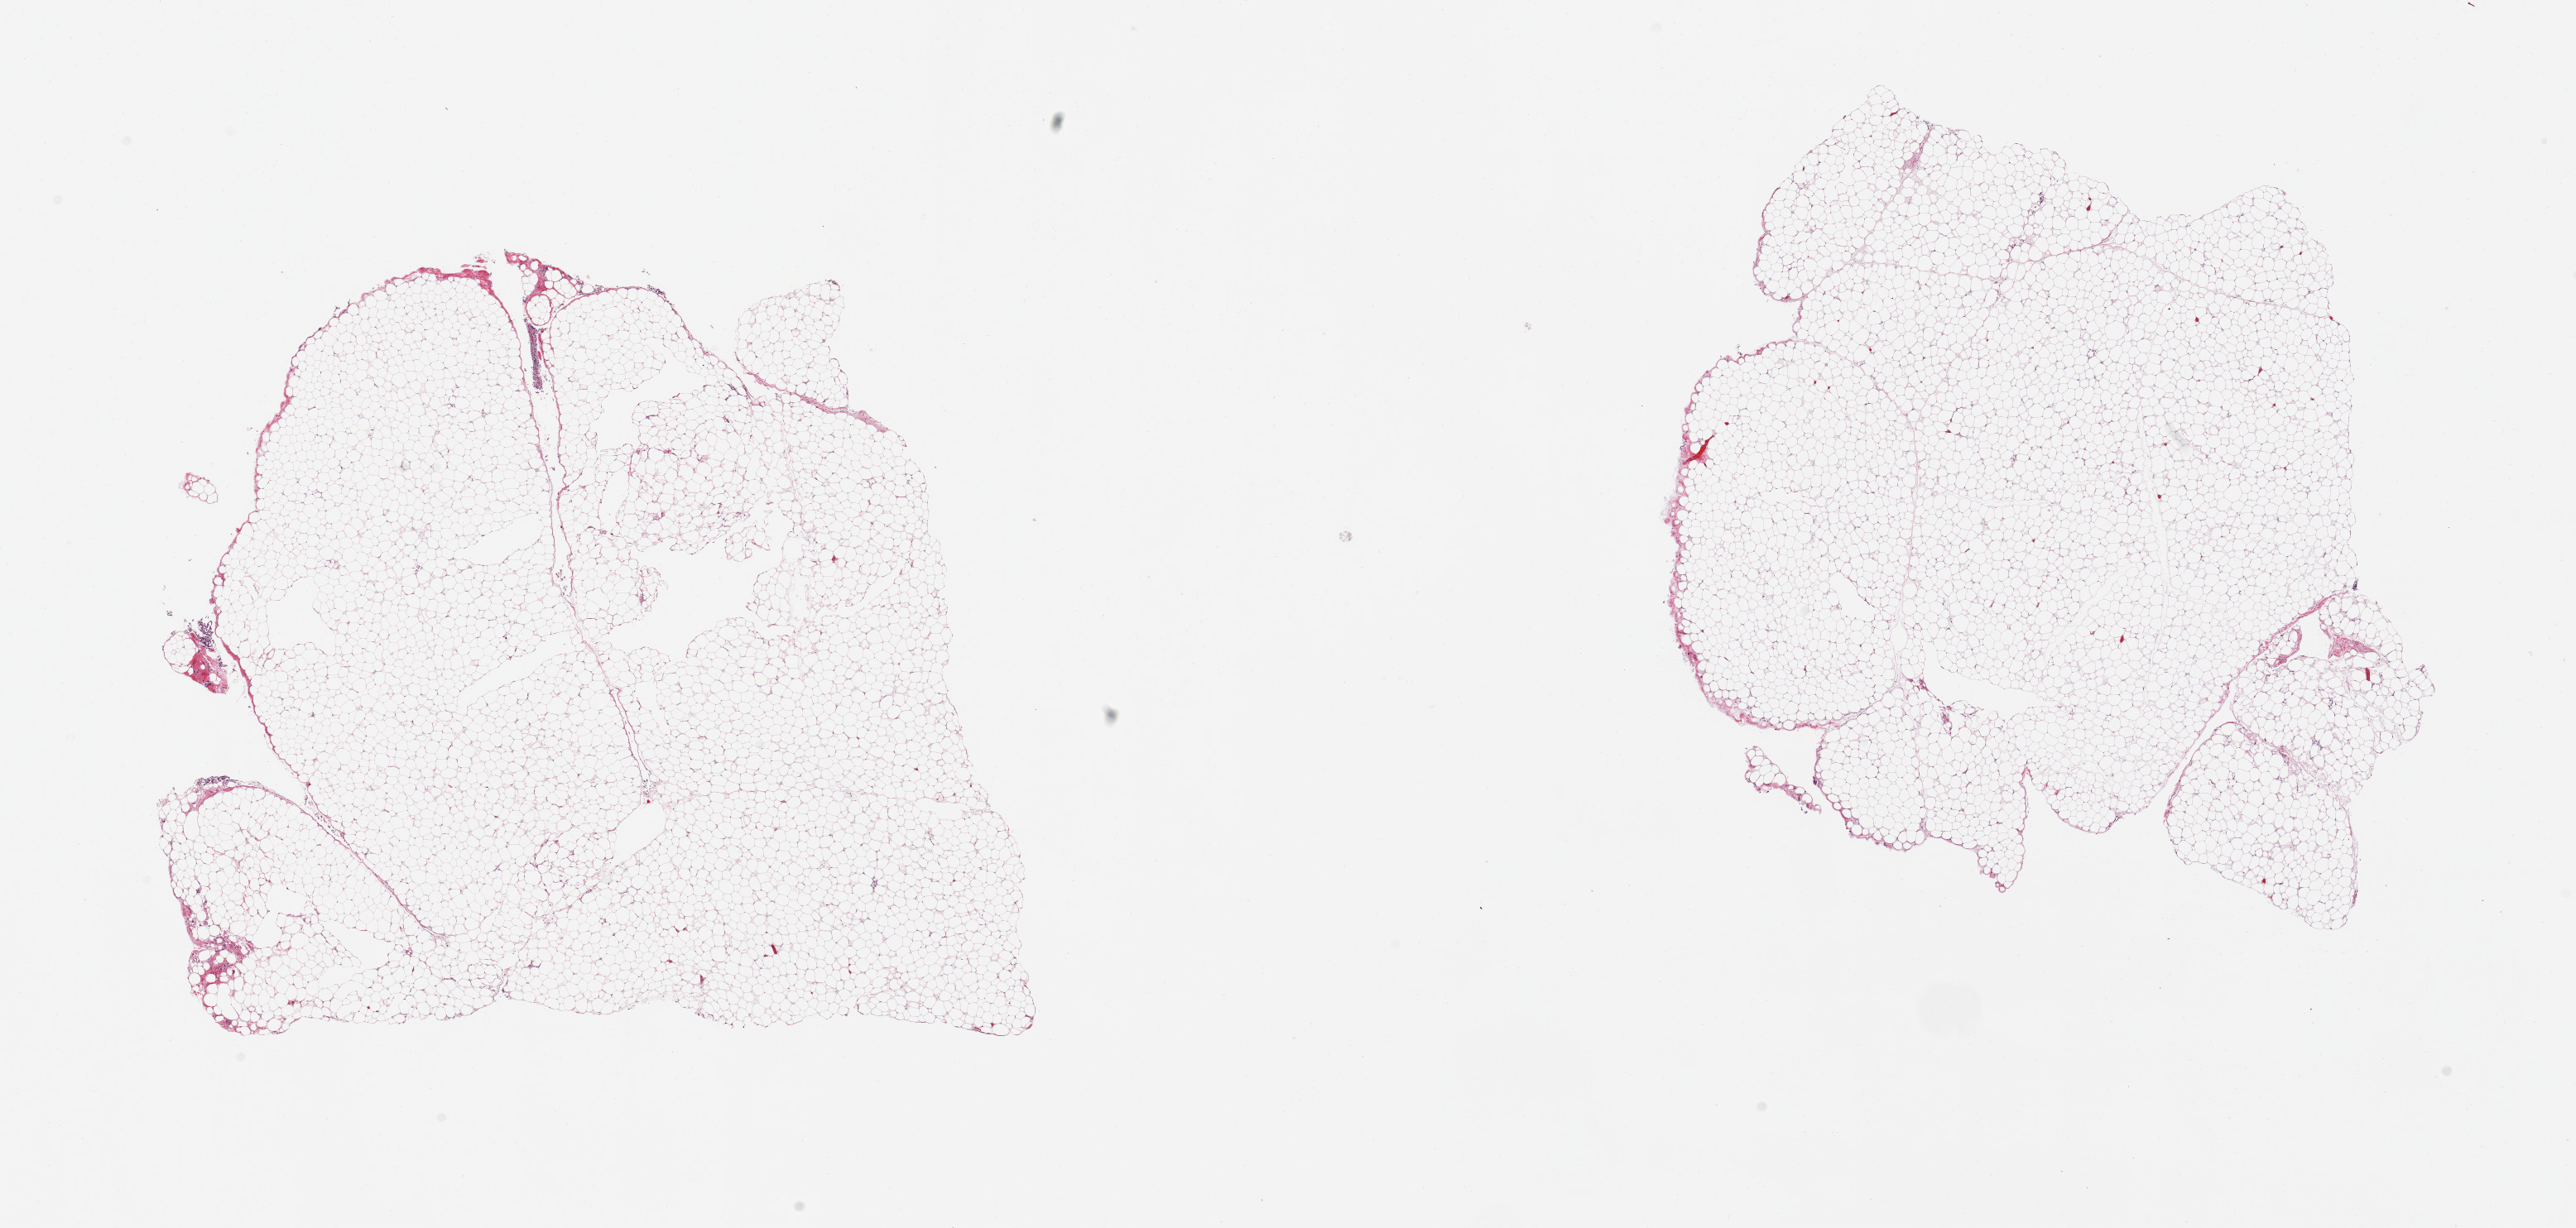
Digitized haematoxylin and eosin-stained section, a low-resolution overview of the entire scanned area, about 24.6 x 11.7 mm (slide scanned at 20x), PAXgene-fixed, paraffin-embedded tissue, target tissue: omentum, tissue donor sample. Donor: male.
Reviewer comment on this tissue sample: 2 pieces, minimal fascia/vascular elements.